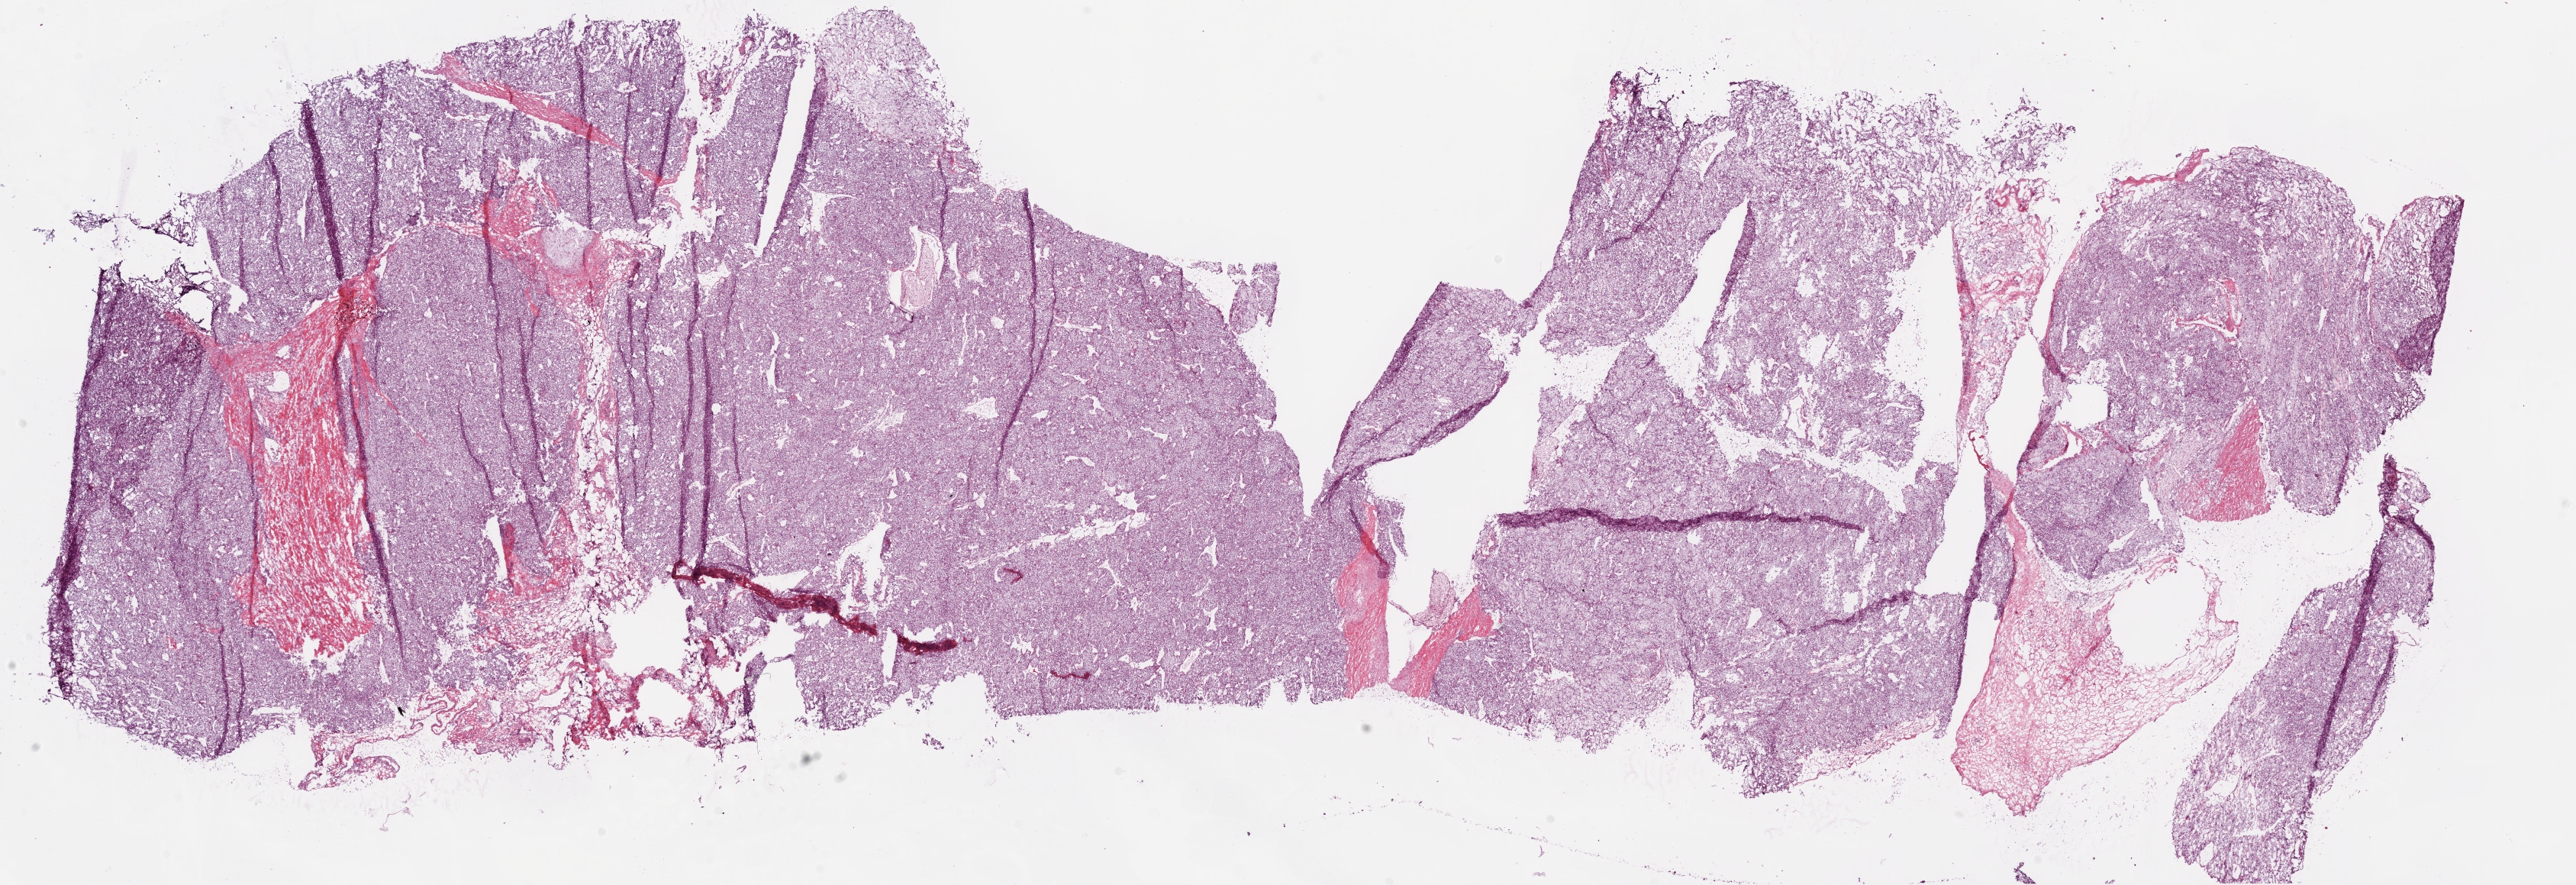
Digitized Hematoxylin and eosin (H&E) stained tissue section (whole slide), low-resolution overview of the scanned area, about 27.1 x 9.3 mm. Frozen section from the bottom of the tissue portion. Primary tumour sample from the kidney. Patient: male, age at initial diagnosis 61 years. Histologic grade: G3 (poorly differentiated). Slide review estimates, as recorded: tumour cells 85%, tumour nuclei 85%, normal cells 0%, stromal cells 15%, necrosis 0%.
* diagnosis: Clear cell adenocarcinoma, NOS
* AJCC pathologic stage: II
* laterality: left